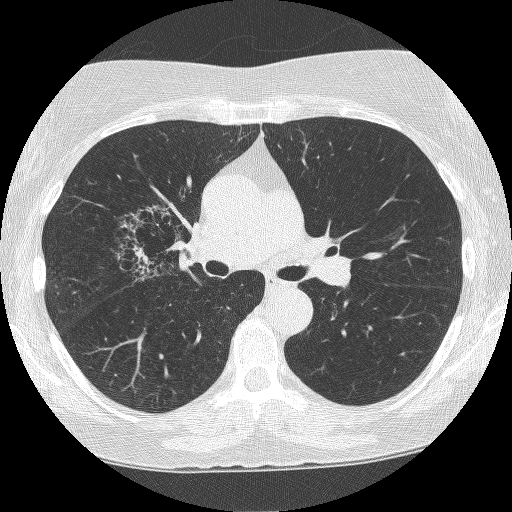
Low-dose screening chest CT, axial slice, second annual screen, lung window (W 1500 / L -600 HU), 1.25 mm slice thickness, slice 147 of 249 in the series. Female, age 64 years at enrolment. Former smoker at enrolment.
- Lesion marked by an expert reader, box from (x=116, y=205) to (x=204, y=288) px.
- The screening reader recorded 4 non-calcified nodules or masses ≥4 mm on this exam (right upper lobe, right upper lobe, right upper lobe, left upper lobe); which of them this box marks is not recorded.
- Official screen result: positive, other.
- Later outcome: lung cancer diagnosed 381 days after this screen (after the third annual screen) — adenocarcinoma, NOS, right upper lobe, right middle lobe, right hilum, stage IV (AJCC 6th edition), 85 mm at pathology.